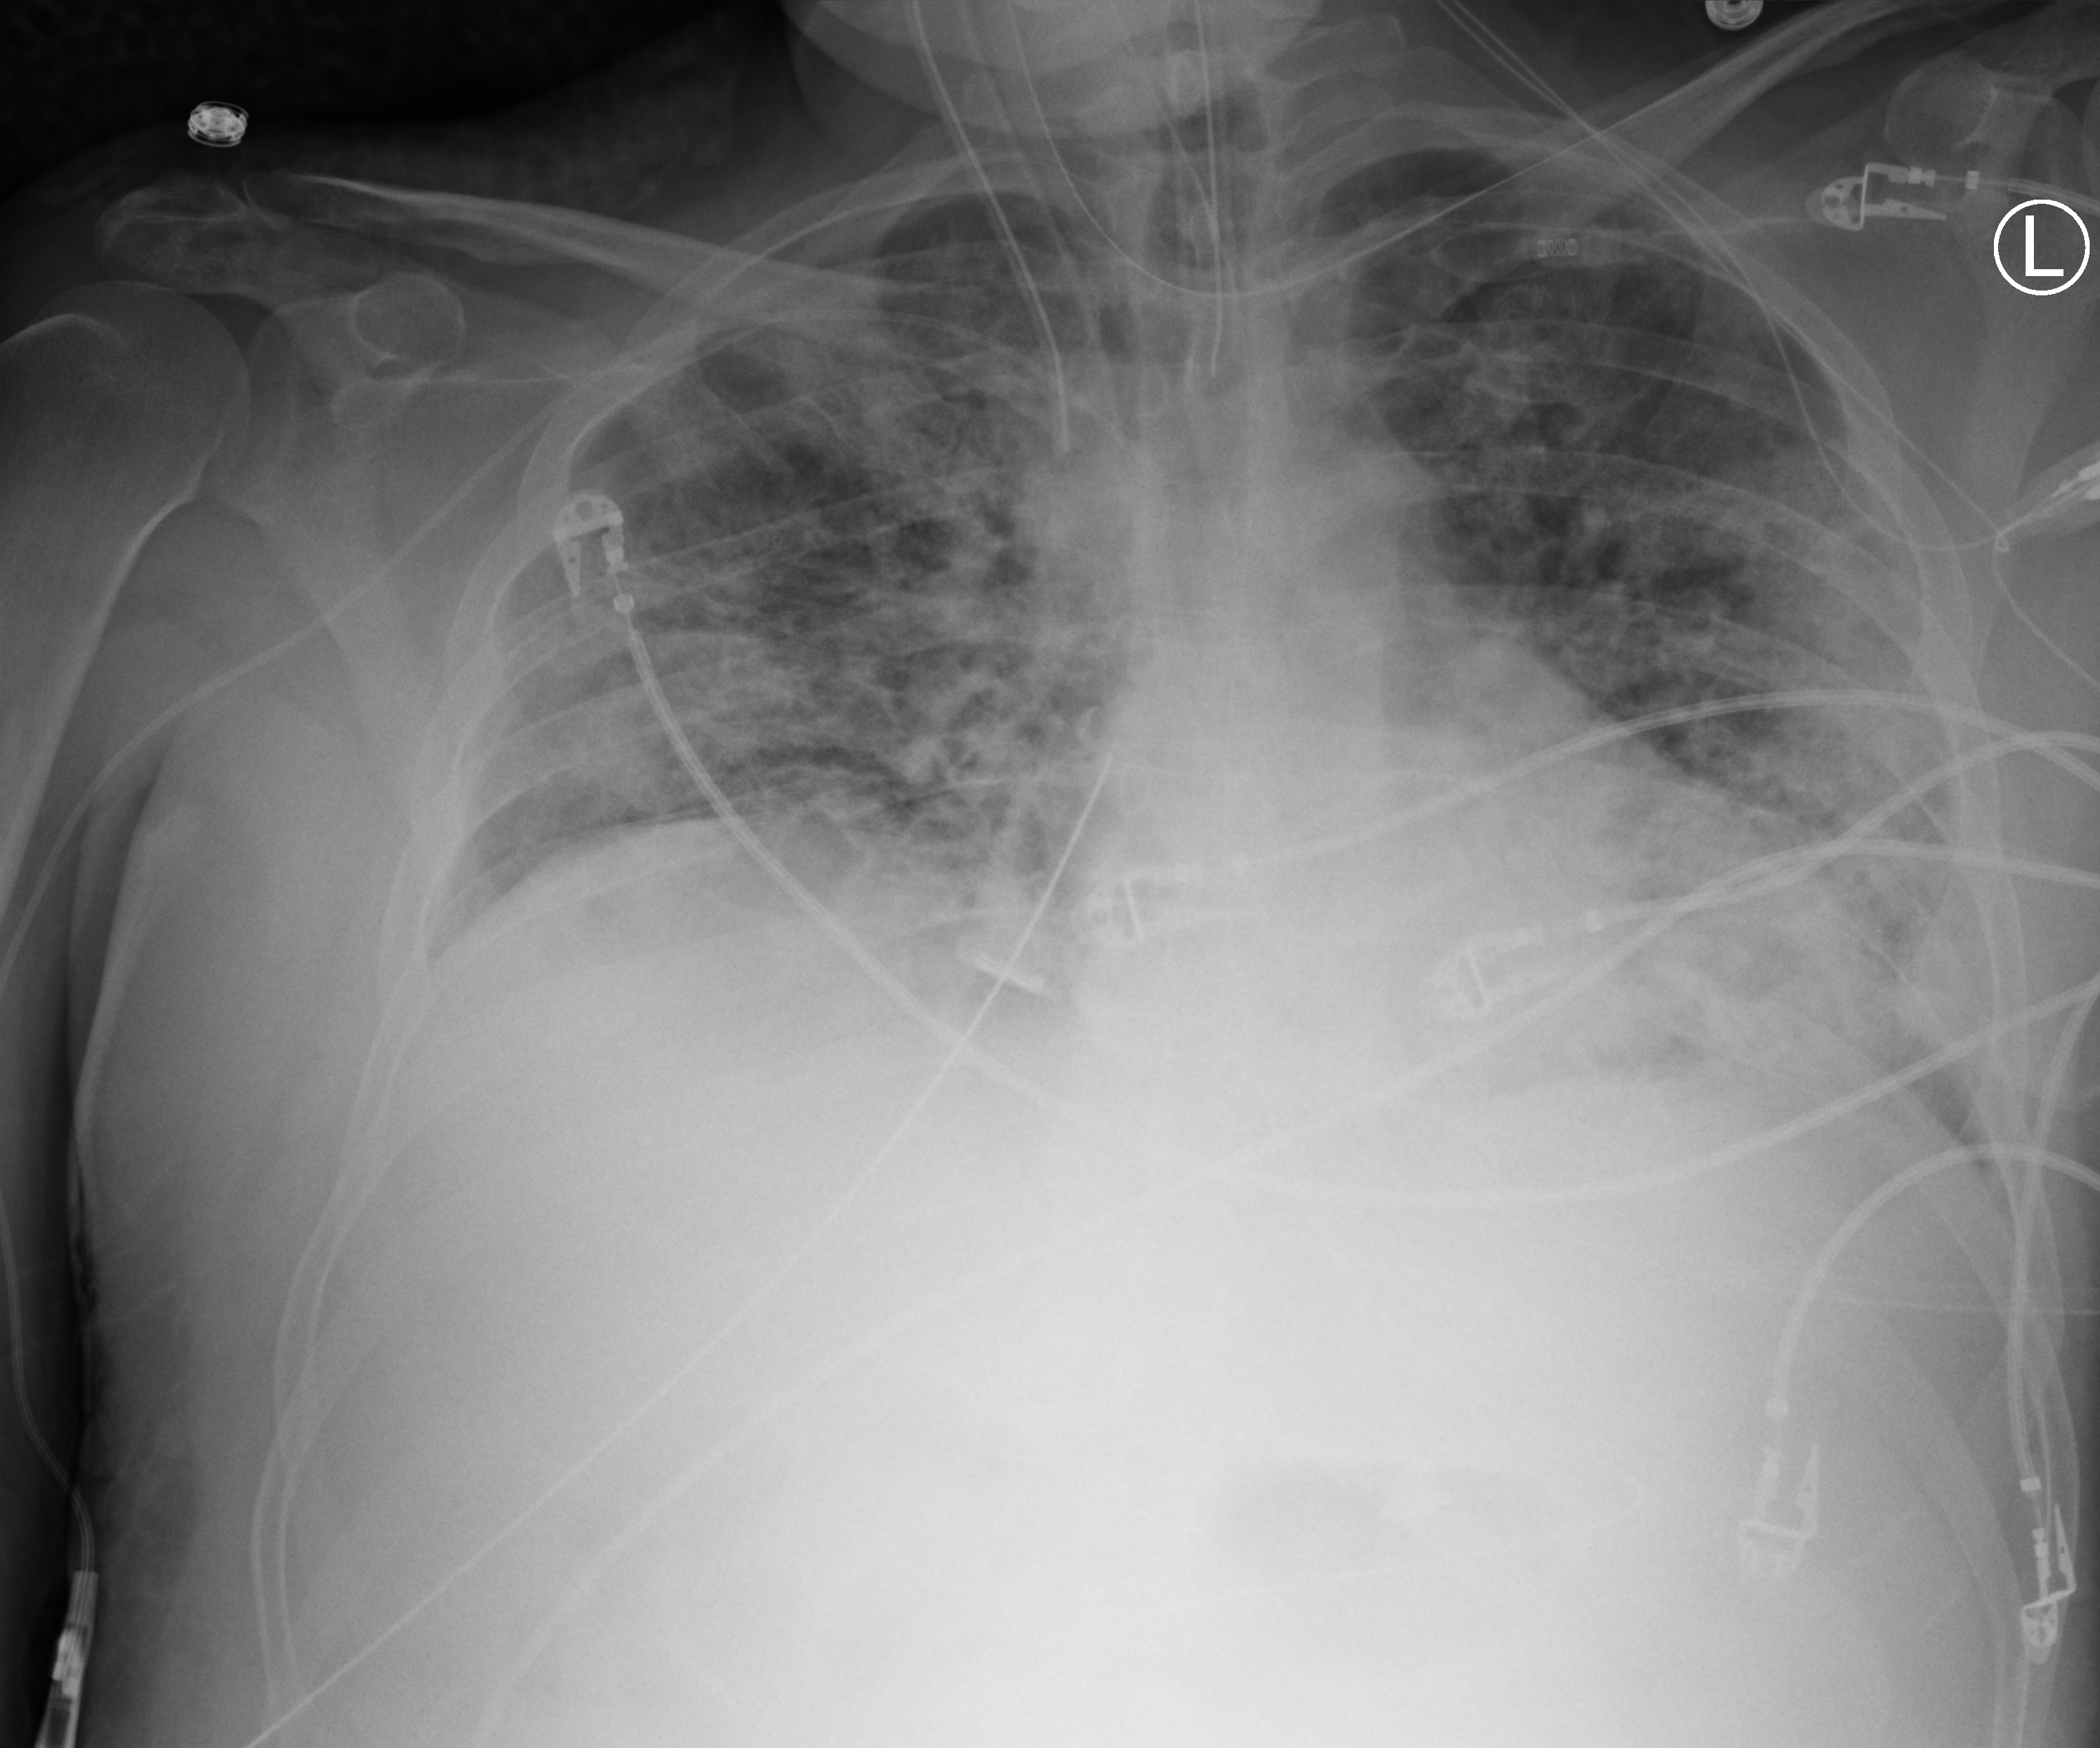
Chest X-ray (portable), anteroposterior (AP) projection. Male patient hospitalised with COVID-19, age 18–59 years.
Admission-level facts for this patient (not findings on this image; timing relative to this image not recorded):
- mechanically ventilated during this hospital stay: yes